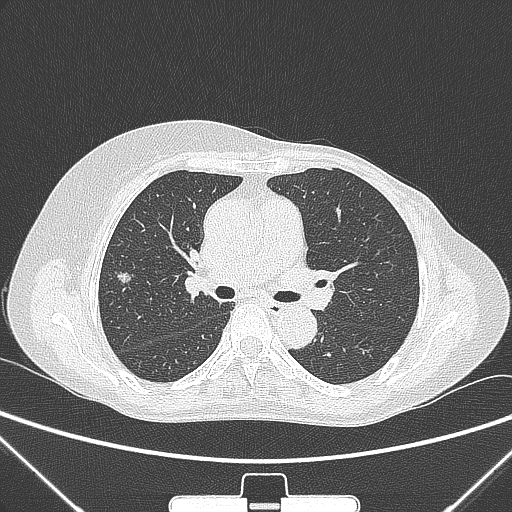
Chest CT, one axial slice. Slice 152 of 265 in the series (ordered by position). Lung window (W 1500 / L -600 HU). 1 mm slice thickness. 512 × 512 image matrix, field of view 350 × 350 mm. Patient: female, 64 years. From the clinical record (not read from this slice): clinical TNM (as recorded): T1c N0 M0; histopathological grade: G1-2.
Outlined on this slice (bounding box drawn by a radiologist):
- lung tumour (recorded histology: adenocarcinoma): bounding box [x1, y1, x2, y2] px = [114, 261, 135, 288]